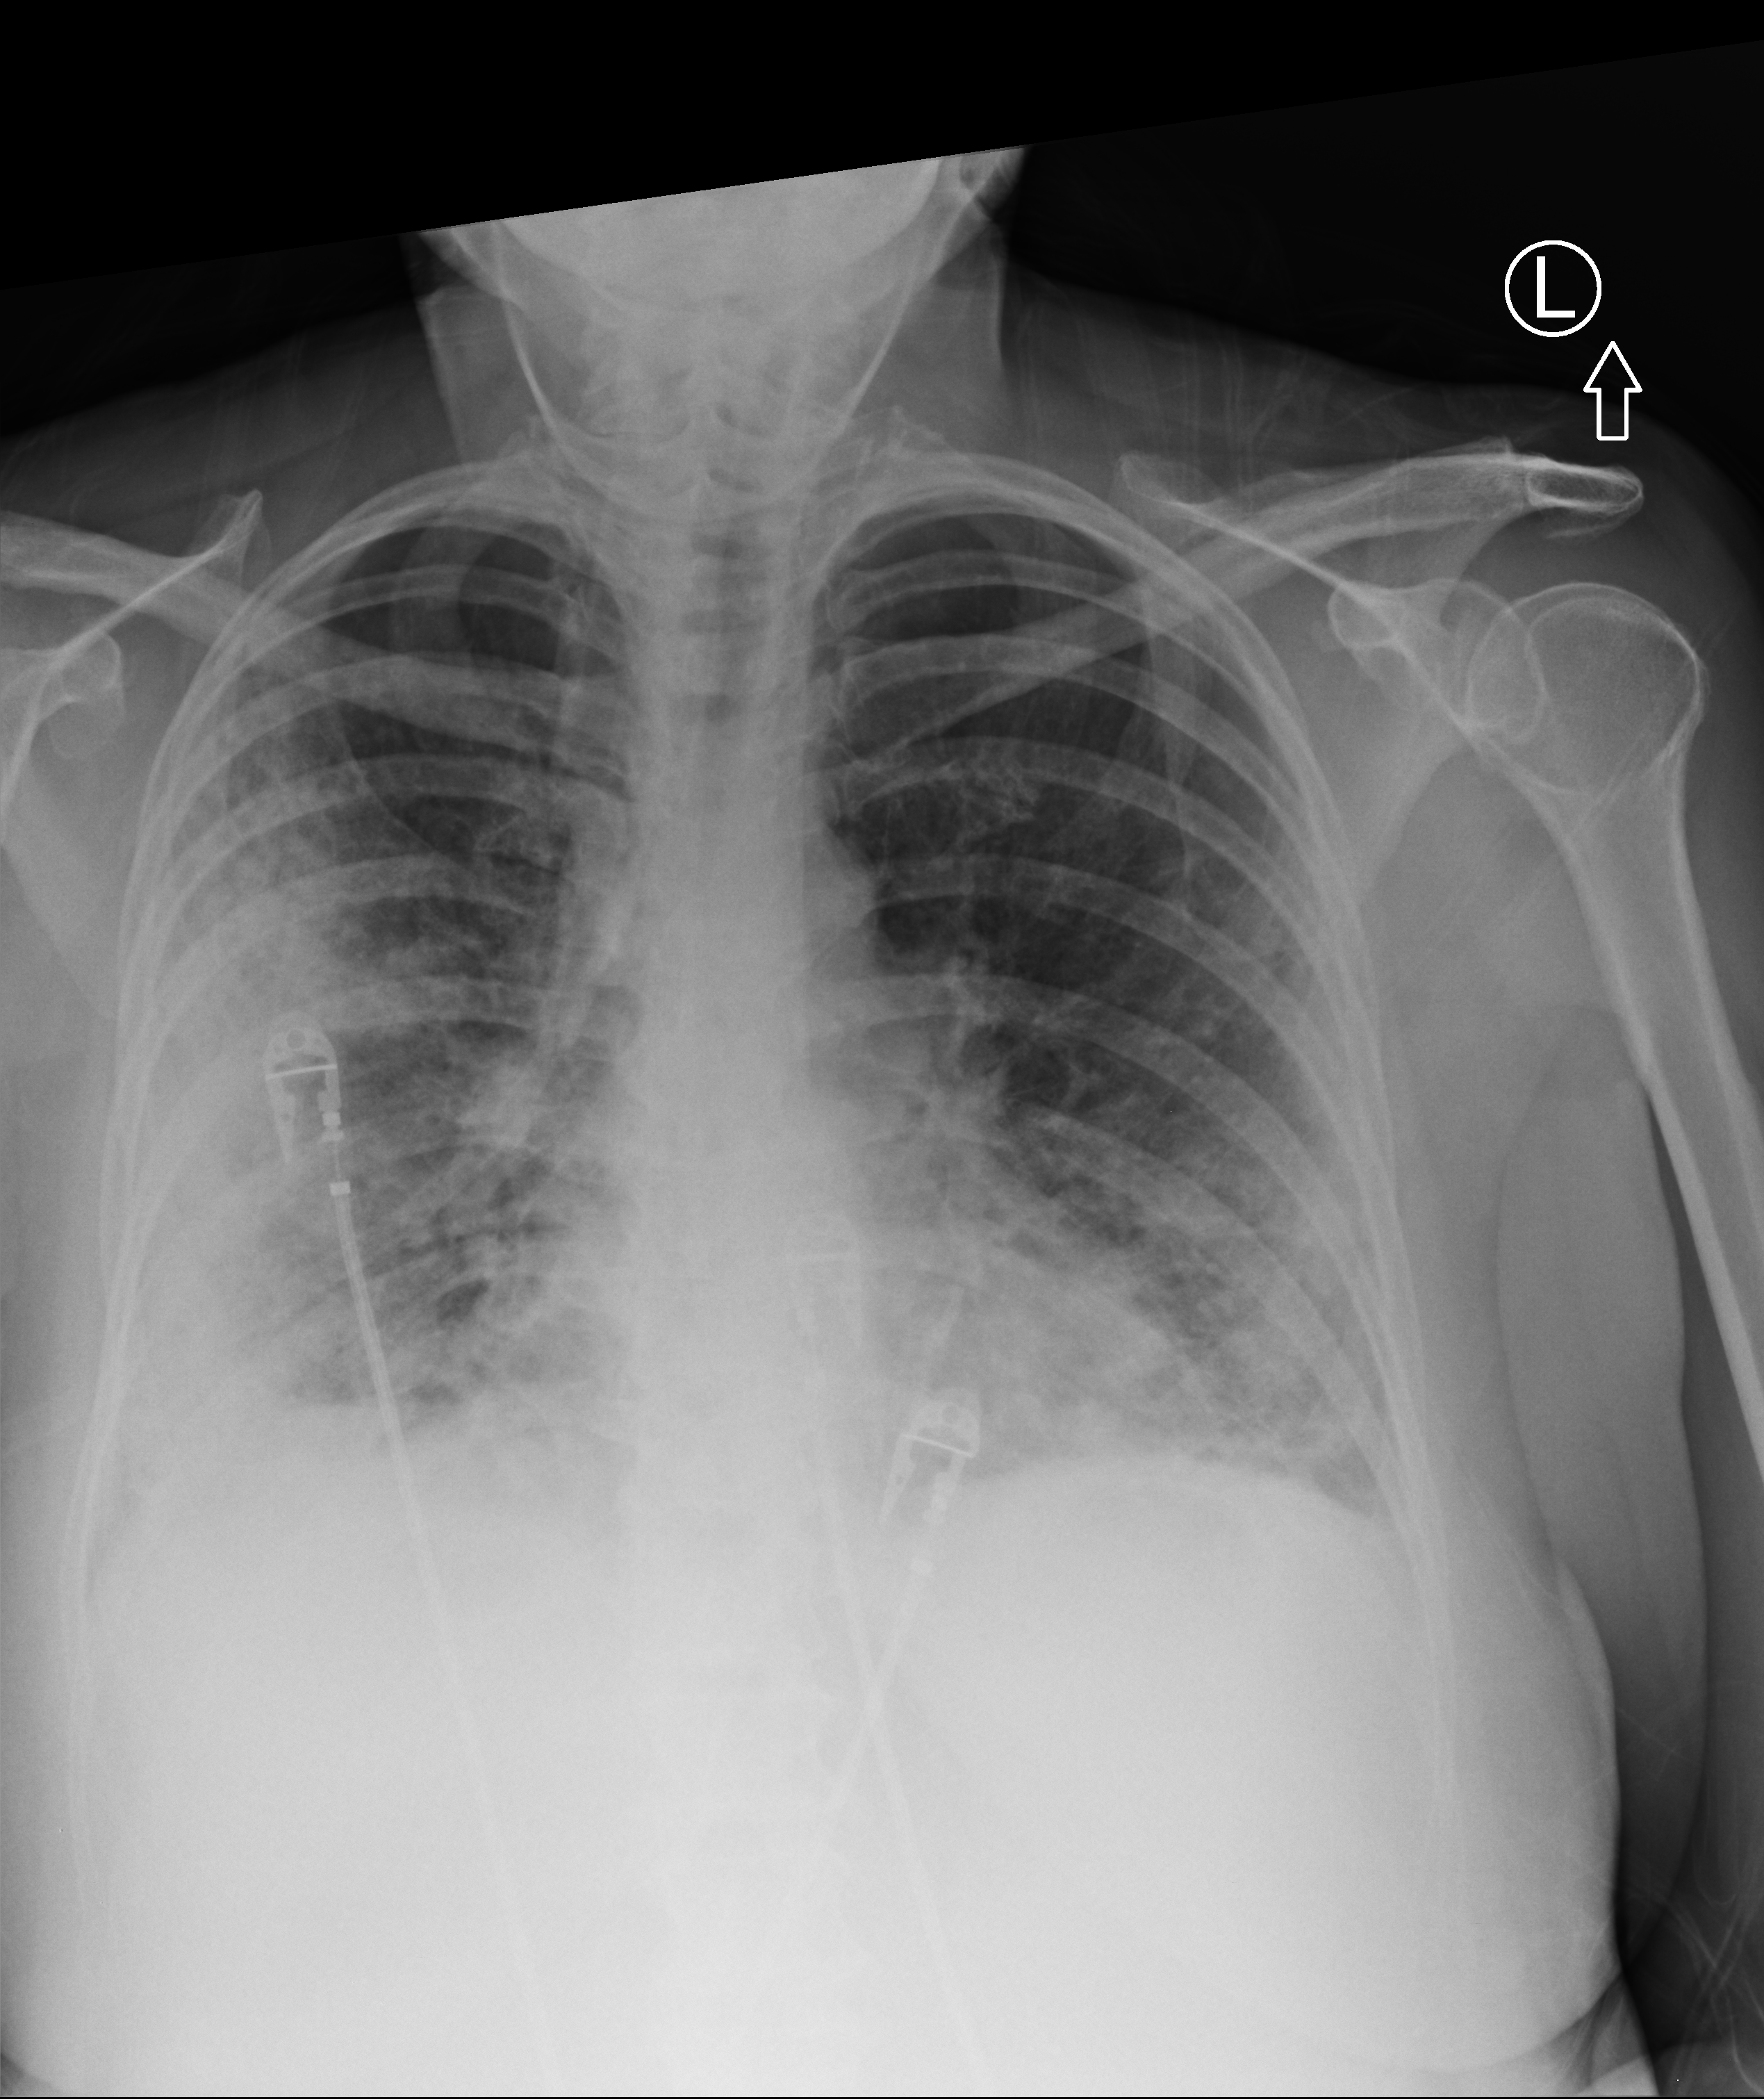
Bedside chest radiograph (computed radiography). Patient hospitalised with COVID-19; female, aged 60–74 years.
From the hospital-stay record, not from the radiograph (when in the stay this image was taken is not recorded): admitted to intensive care during this hospital stay: no; mechanically ventilated during this hospital stay: no.